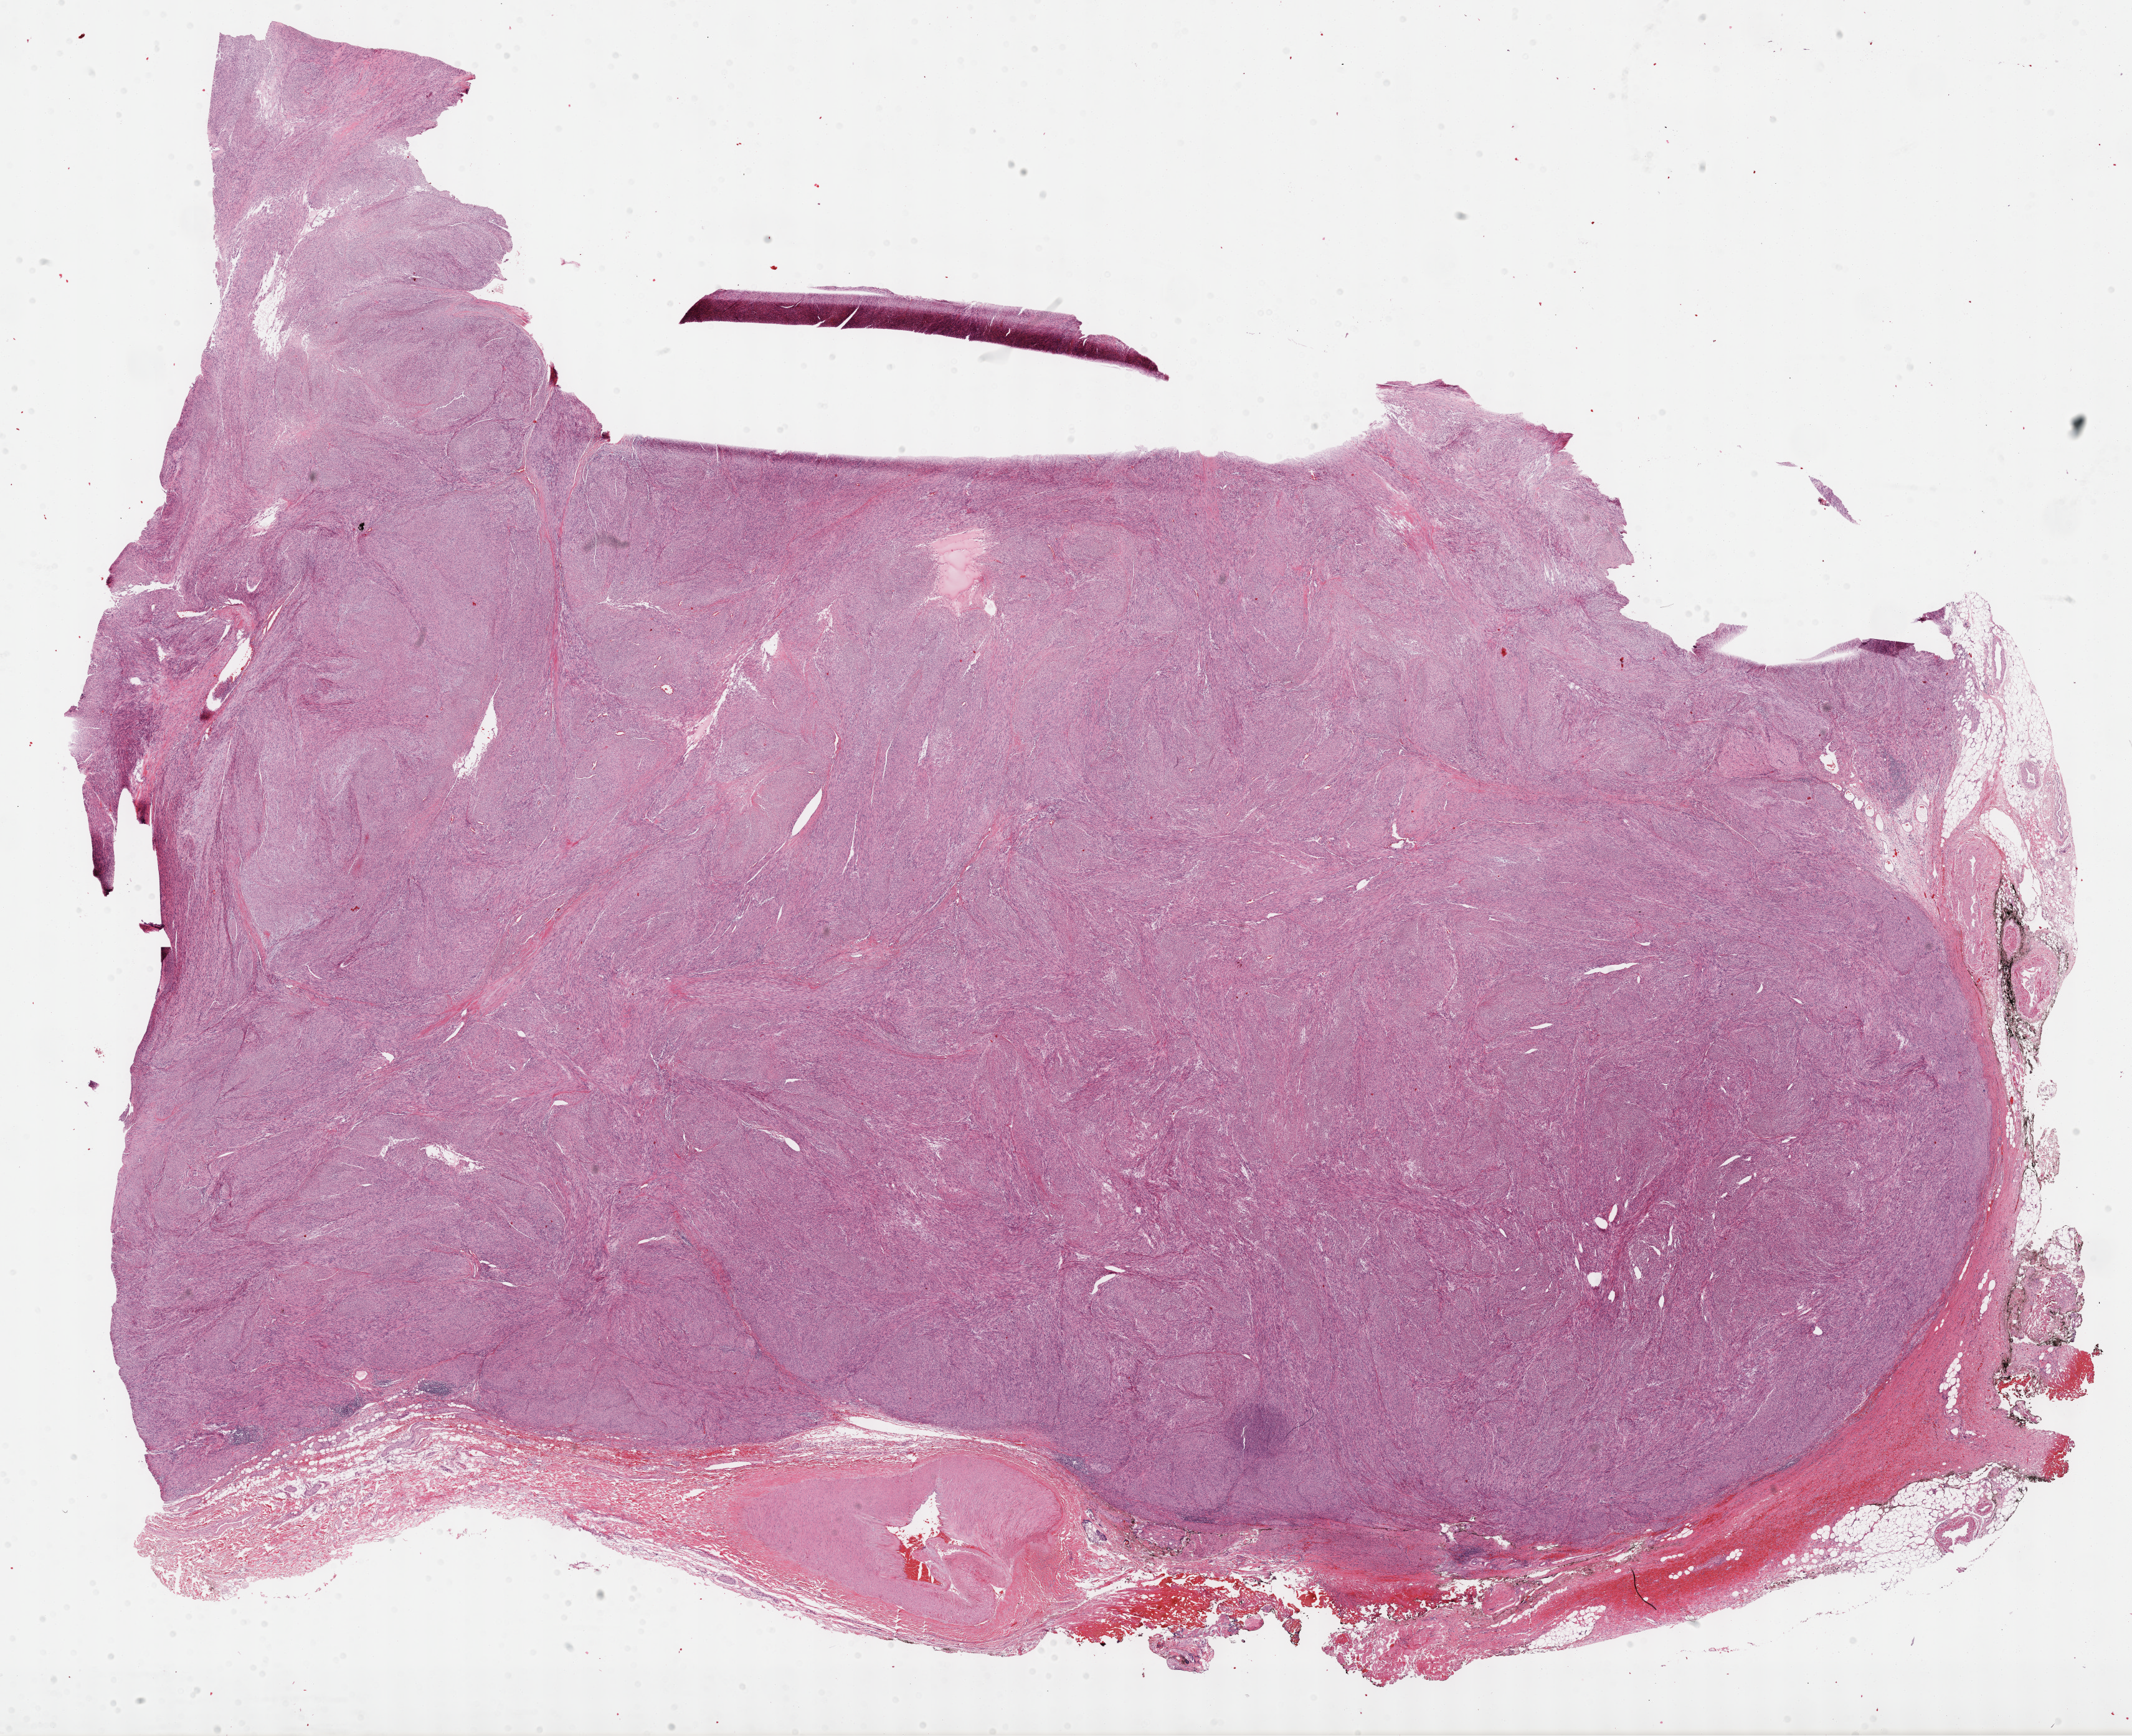
Whole-slide histology image, Hematoxylin and eosin (H&E) stained, shown as a low-resolution overview of the whole scanned area (about 27.7 x 22.5 mm, slide scanned at 40x). FFPE section. Sample: primary tumour, retroperitoneum and peritoneum. Female, age 78 years at initial diagnosis.
* histologic diagnosis: Dedifferentiated liposarcoma